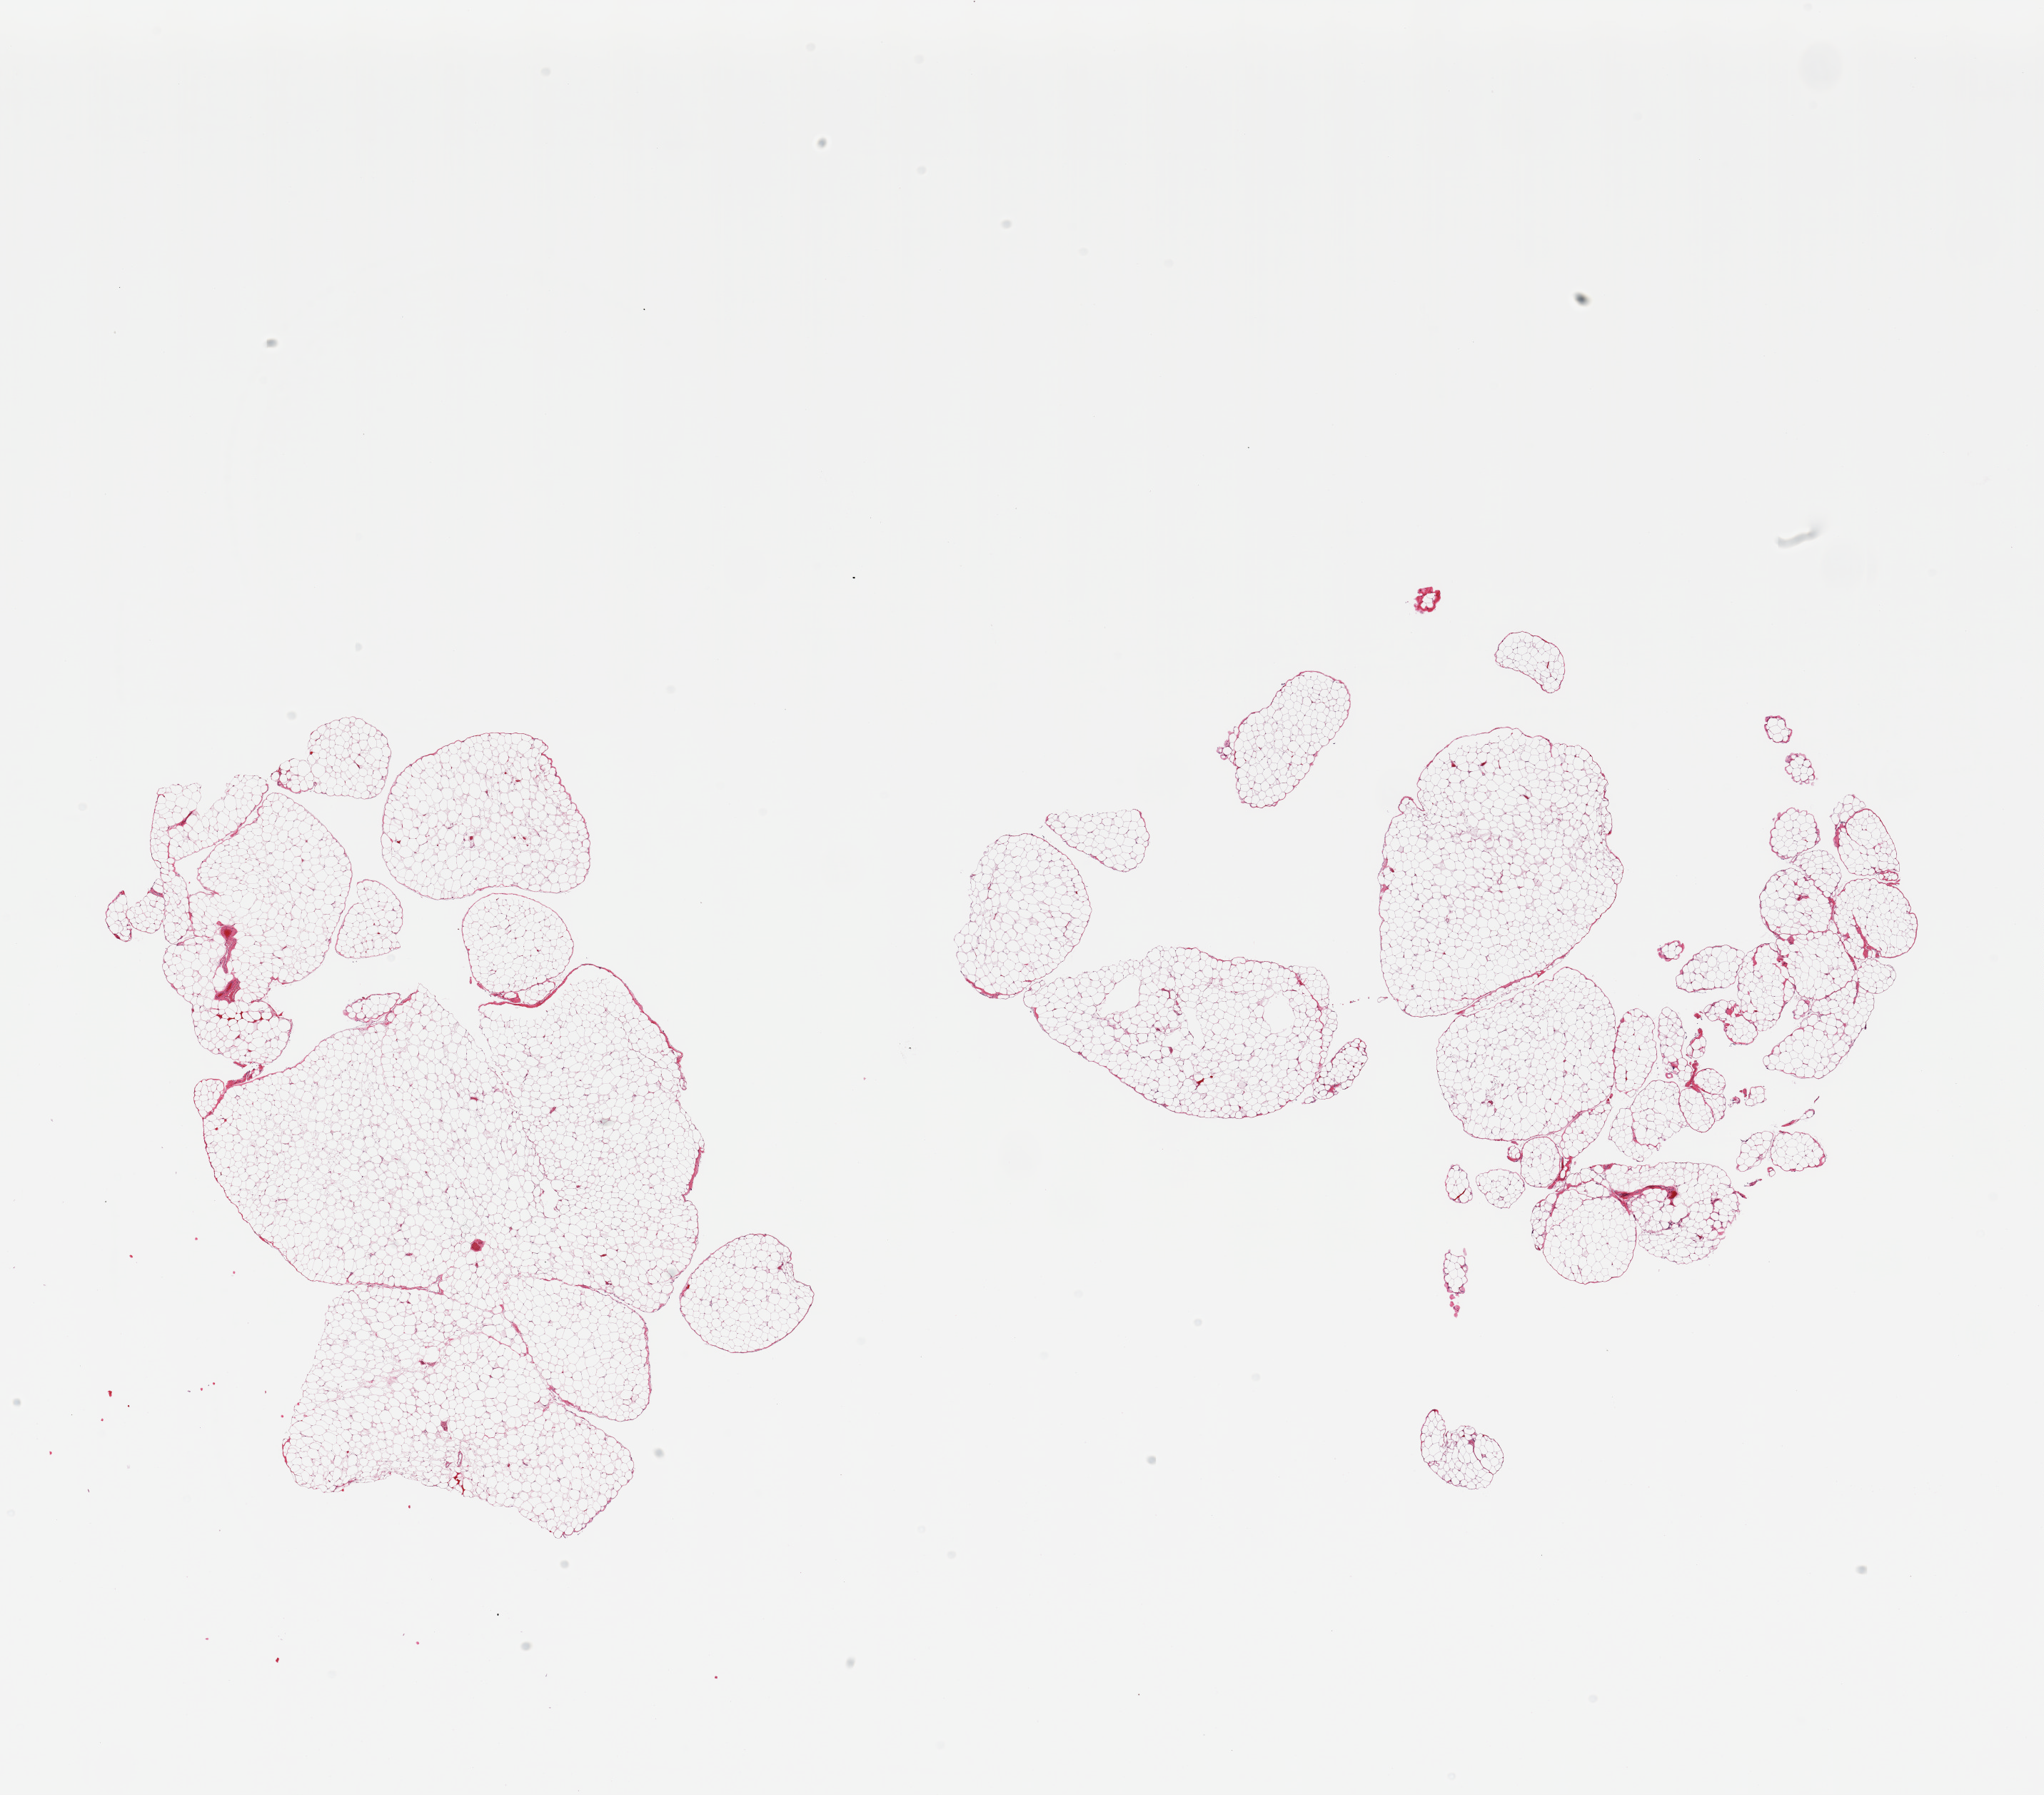
Digitized H&E-stained section, brightfield, a low-resolution overview of the entire scanned area, about 22.6 x 19.9 mm. PAXgene-fixed paraffin-embedded (PFPE) section. Section of omentum (target tissue). Donor tissue sample. Donor: male.
- reviewer comment on this tissue sample: 2 pieces, trace fascia/vascular elements